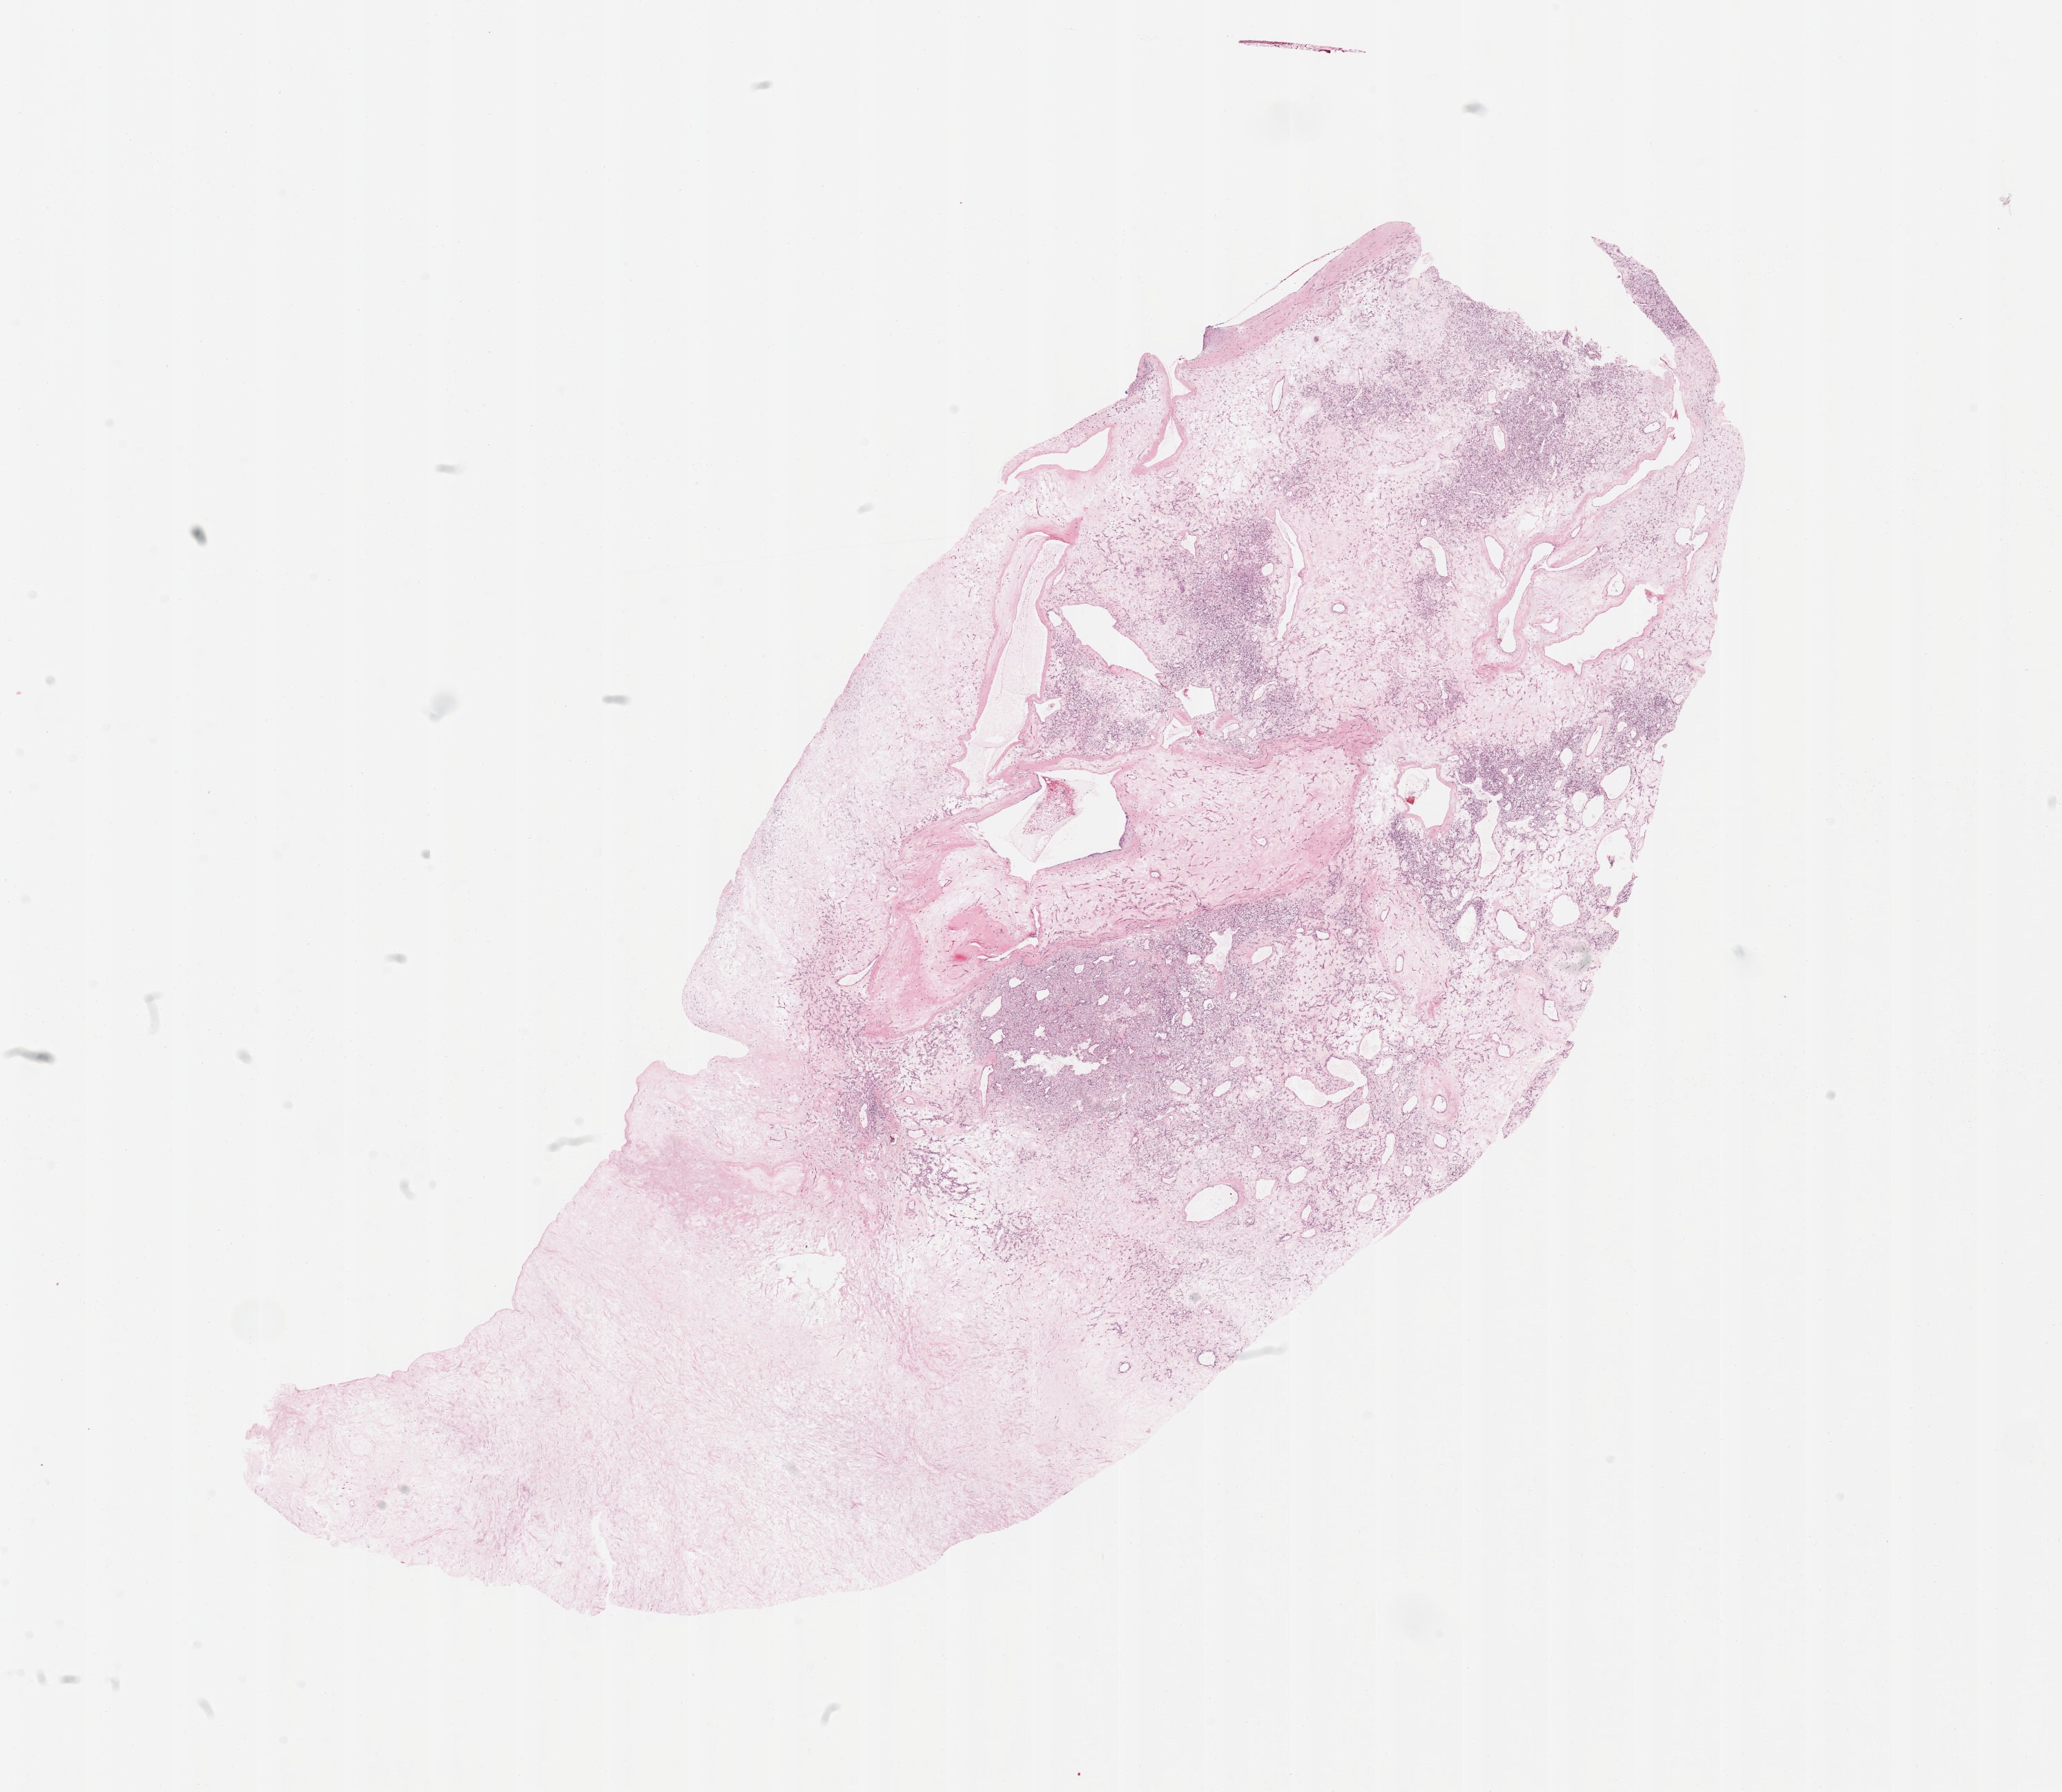
Hematoxylin and eosin (H&E) stained whole-slide image — a low-resolution overview of the entire scanned area, about 23.6 x 20.5 mm (slide scanned at 20x). Tumour tissue sample, sampled site: kidney. 67-year-old male patient. Histologic grade: G4 (undifferentiated). Slide review estimates, as recorded: tumour nuclei 80%, necrosis 5%.
* primary tumour site (as recorded): upper pole
* diagnosis: Renal cell carcinoma, NOS
* AJCC pathologic stage: III